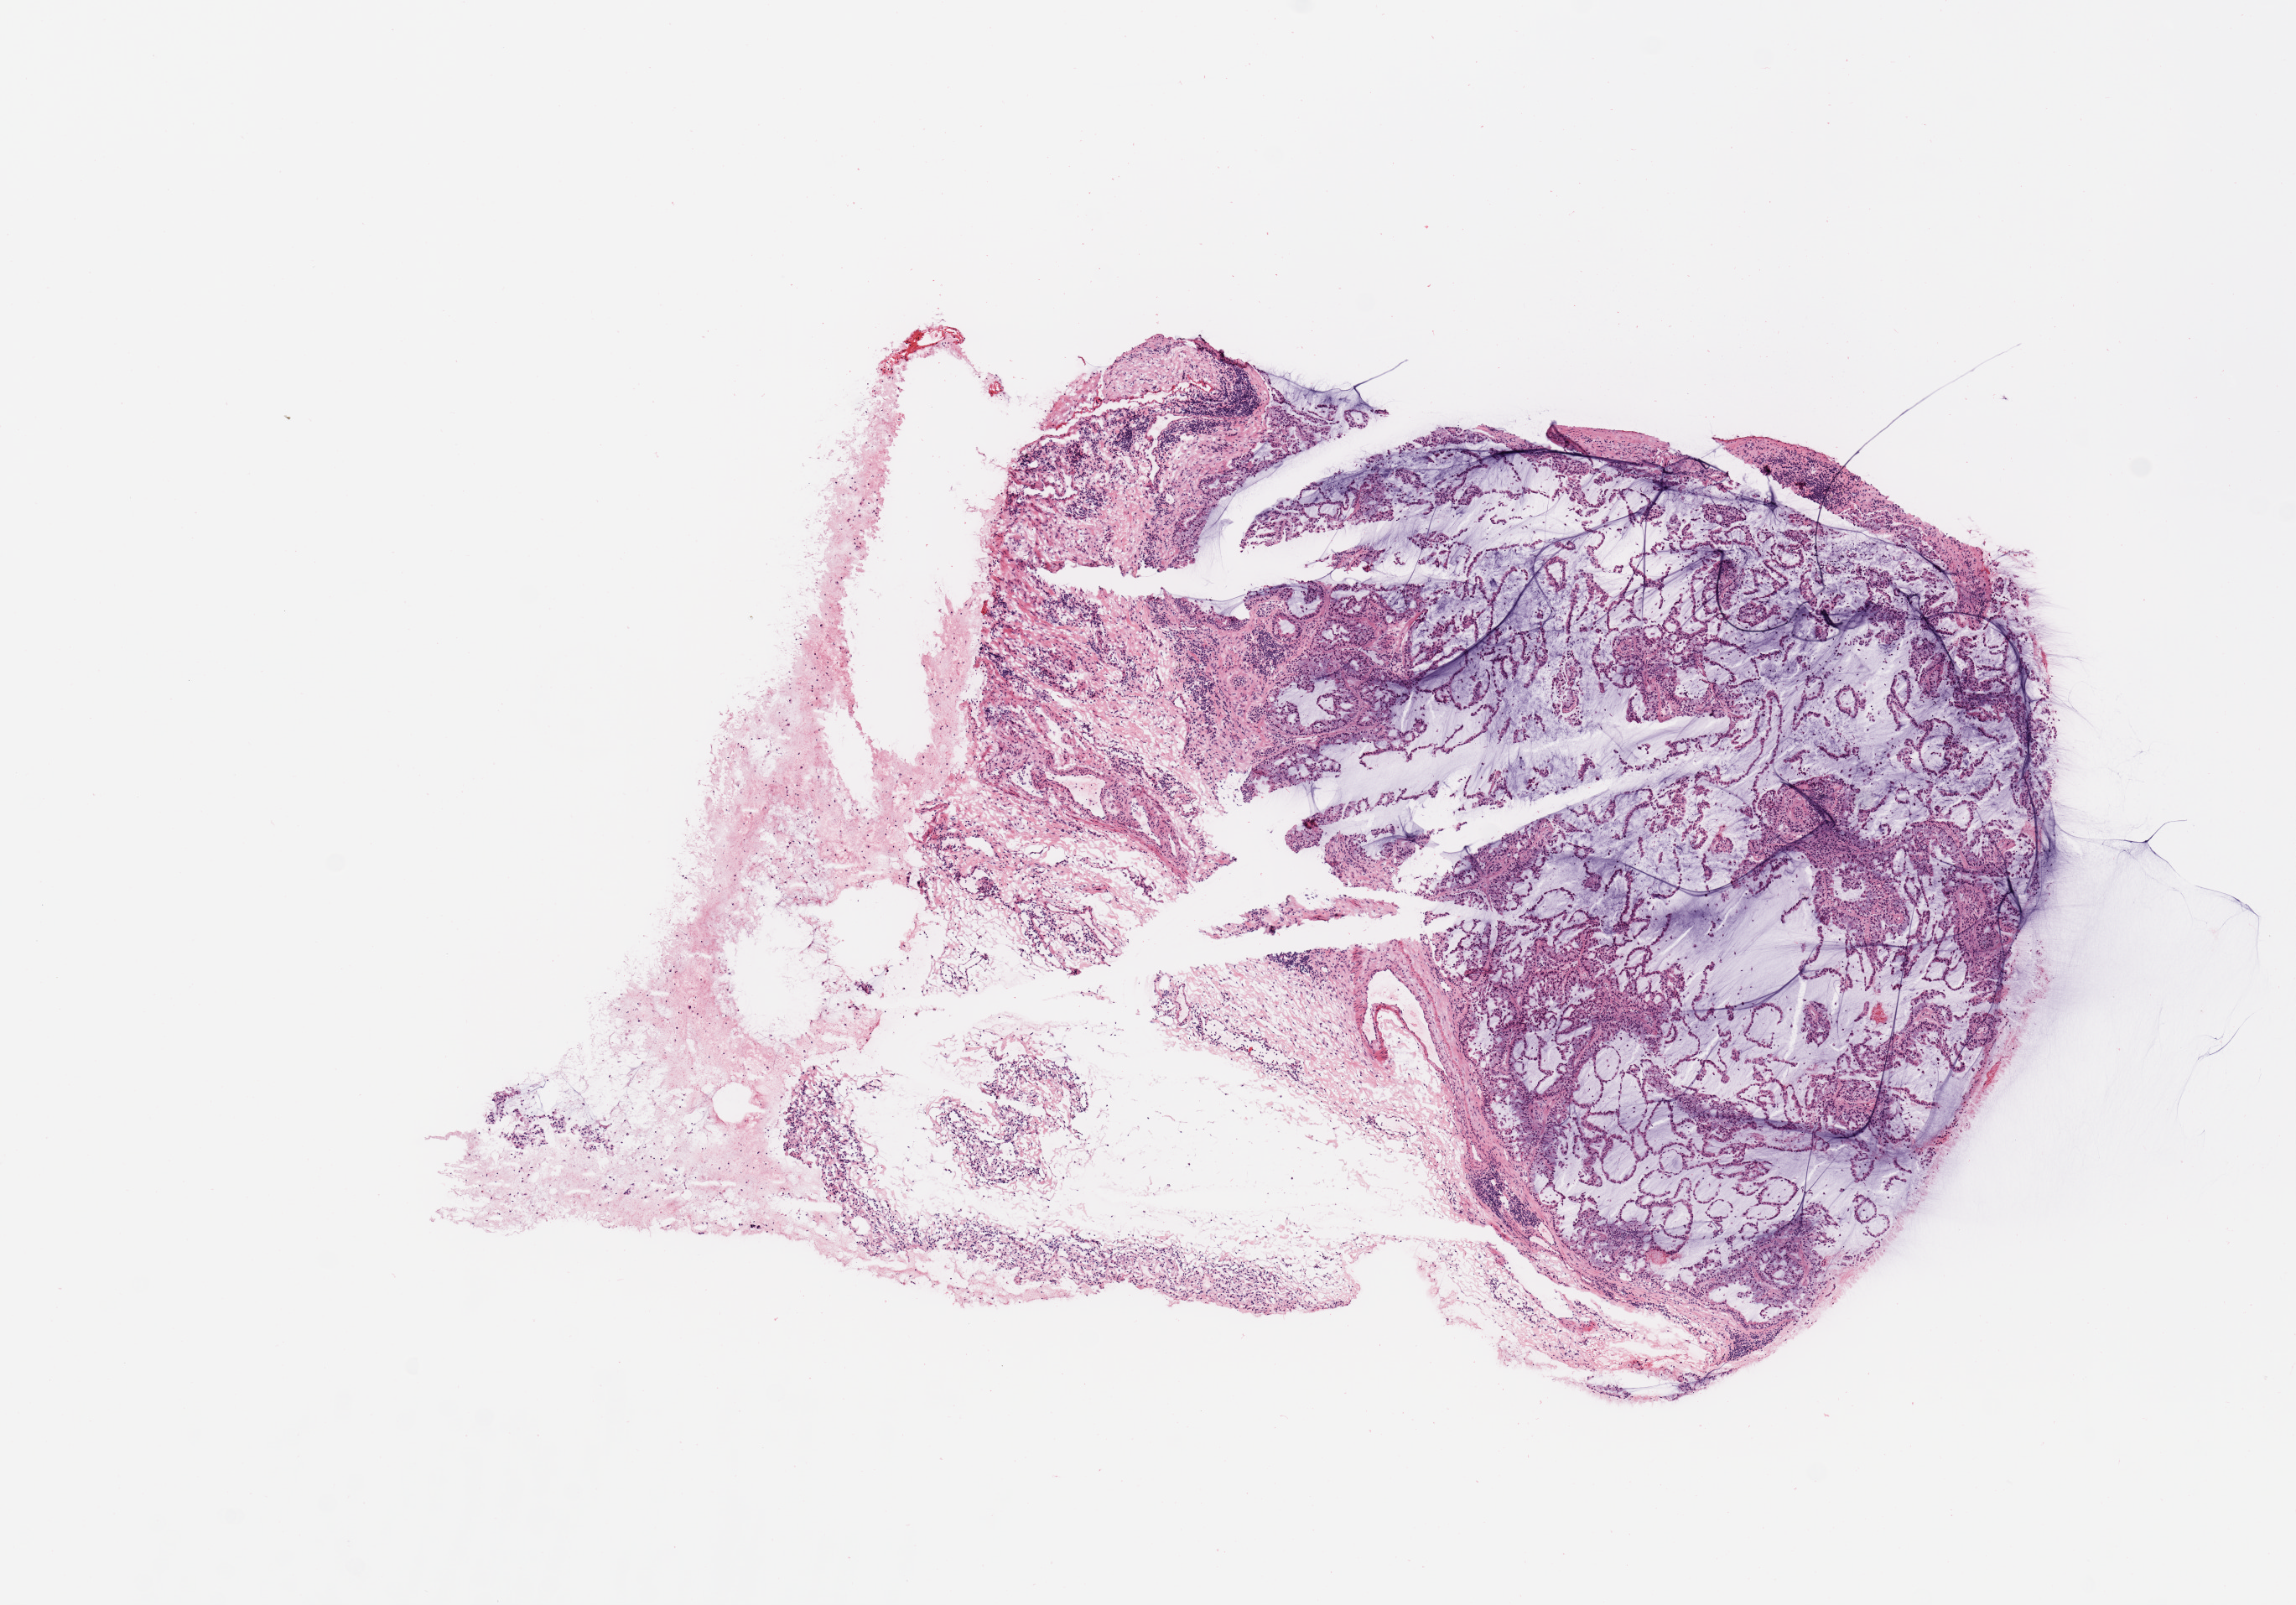
H&E-stained whole-slide image — shown as a low-resolution overview of the whole scanned area (about 10.8 x 7.6 mm, slide scanned at 20x), tumour tissue sample, sampled site: lung. Patient: female, age 35 years. Histologic grade: G3 (poorly differentiated). Slide review estimates, as recorded: tumour nuclei 60%, necrosis 10%.
AJCC pathologic stage: IB. Diagnosis: Adenocarcinoma, NOS. Primary tumour site (as recorded): left lower lobe.